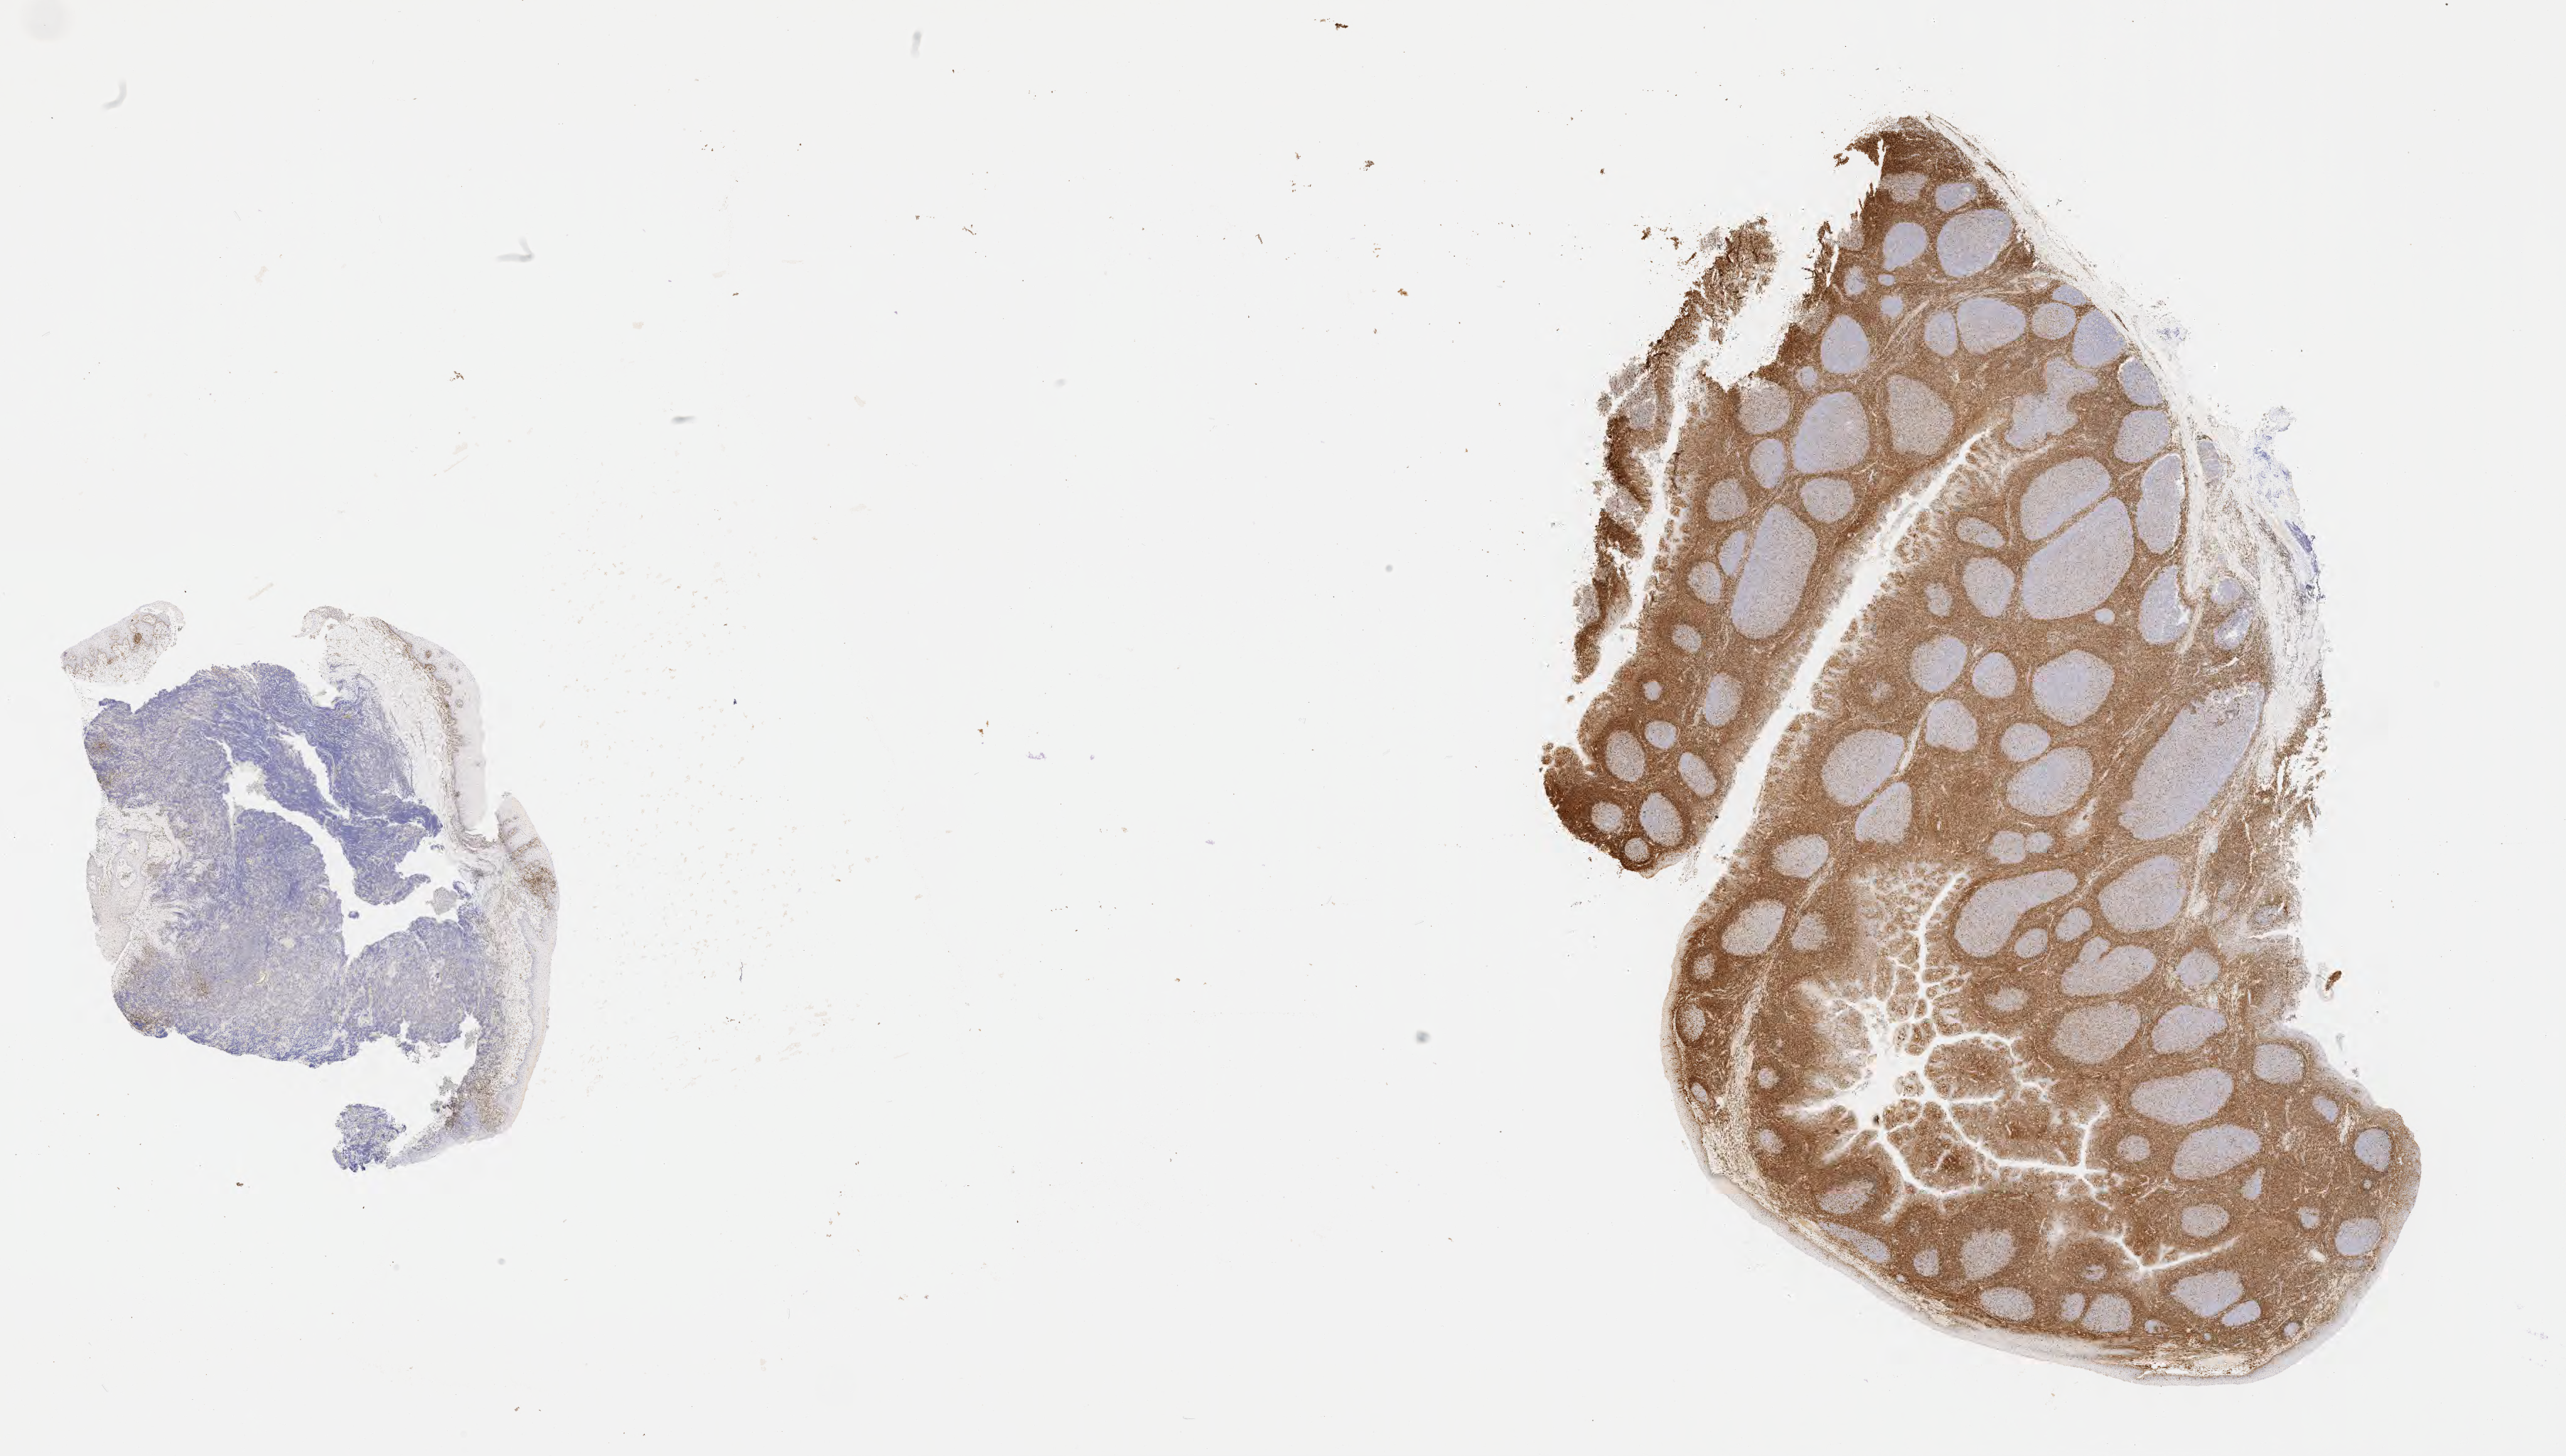
Whole-slide image, immunohistochemical stain for BCL2 — shown as a low-resolution overview of the whole scanned area (about 29.2 x 16.6 mm), tumor tissue, anatomic site: mandible. Female patient; age at initial diagnosis 7 years.
- diagnosis: Burkitt lymphoma, NOS